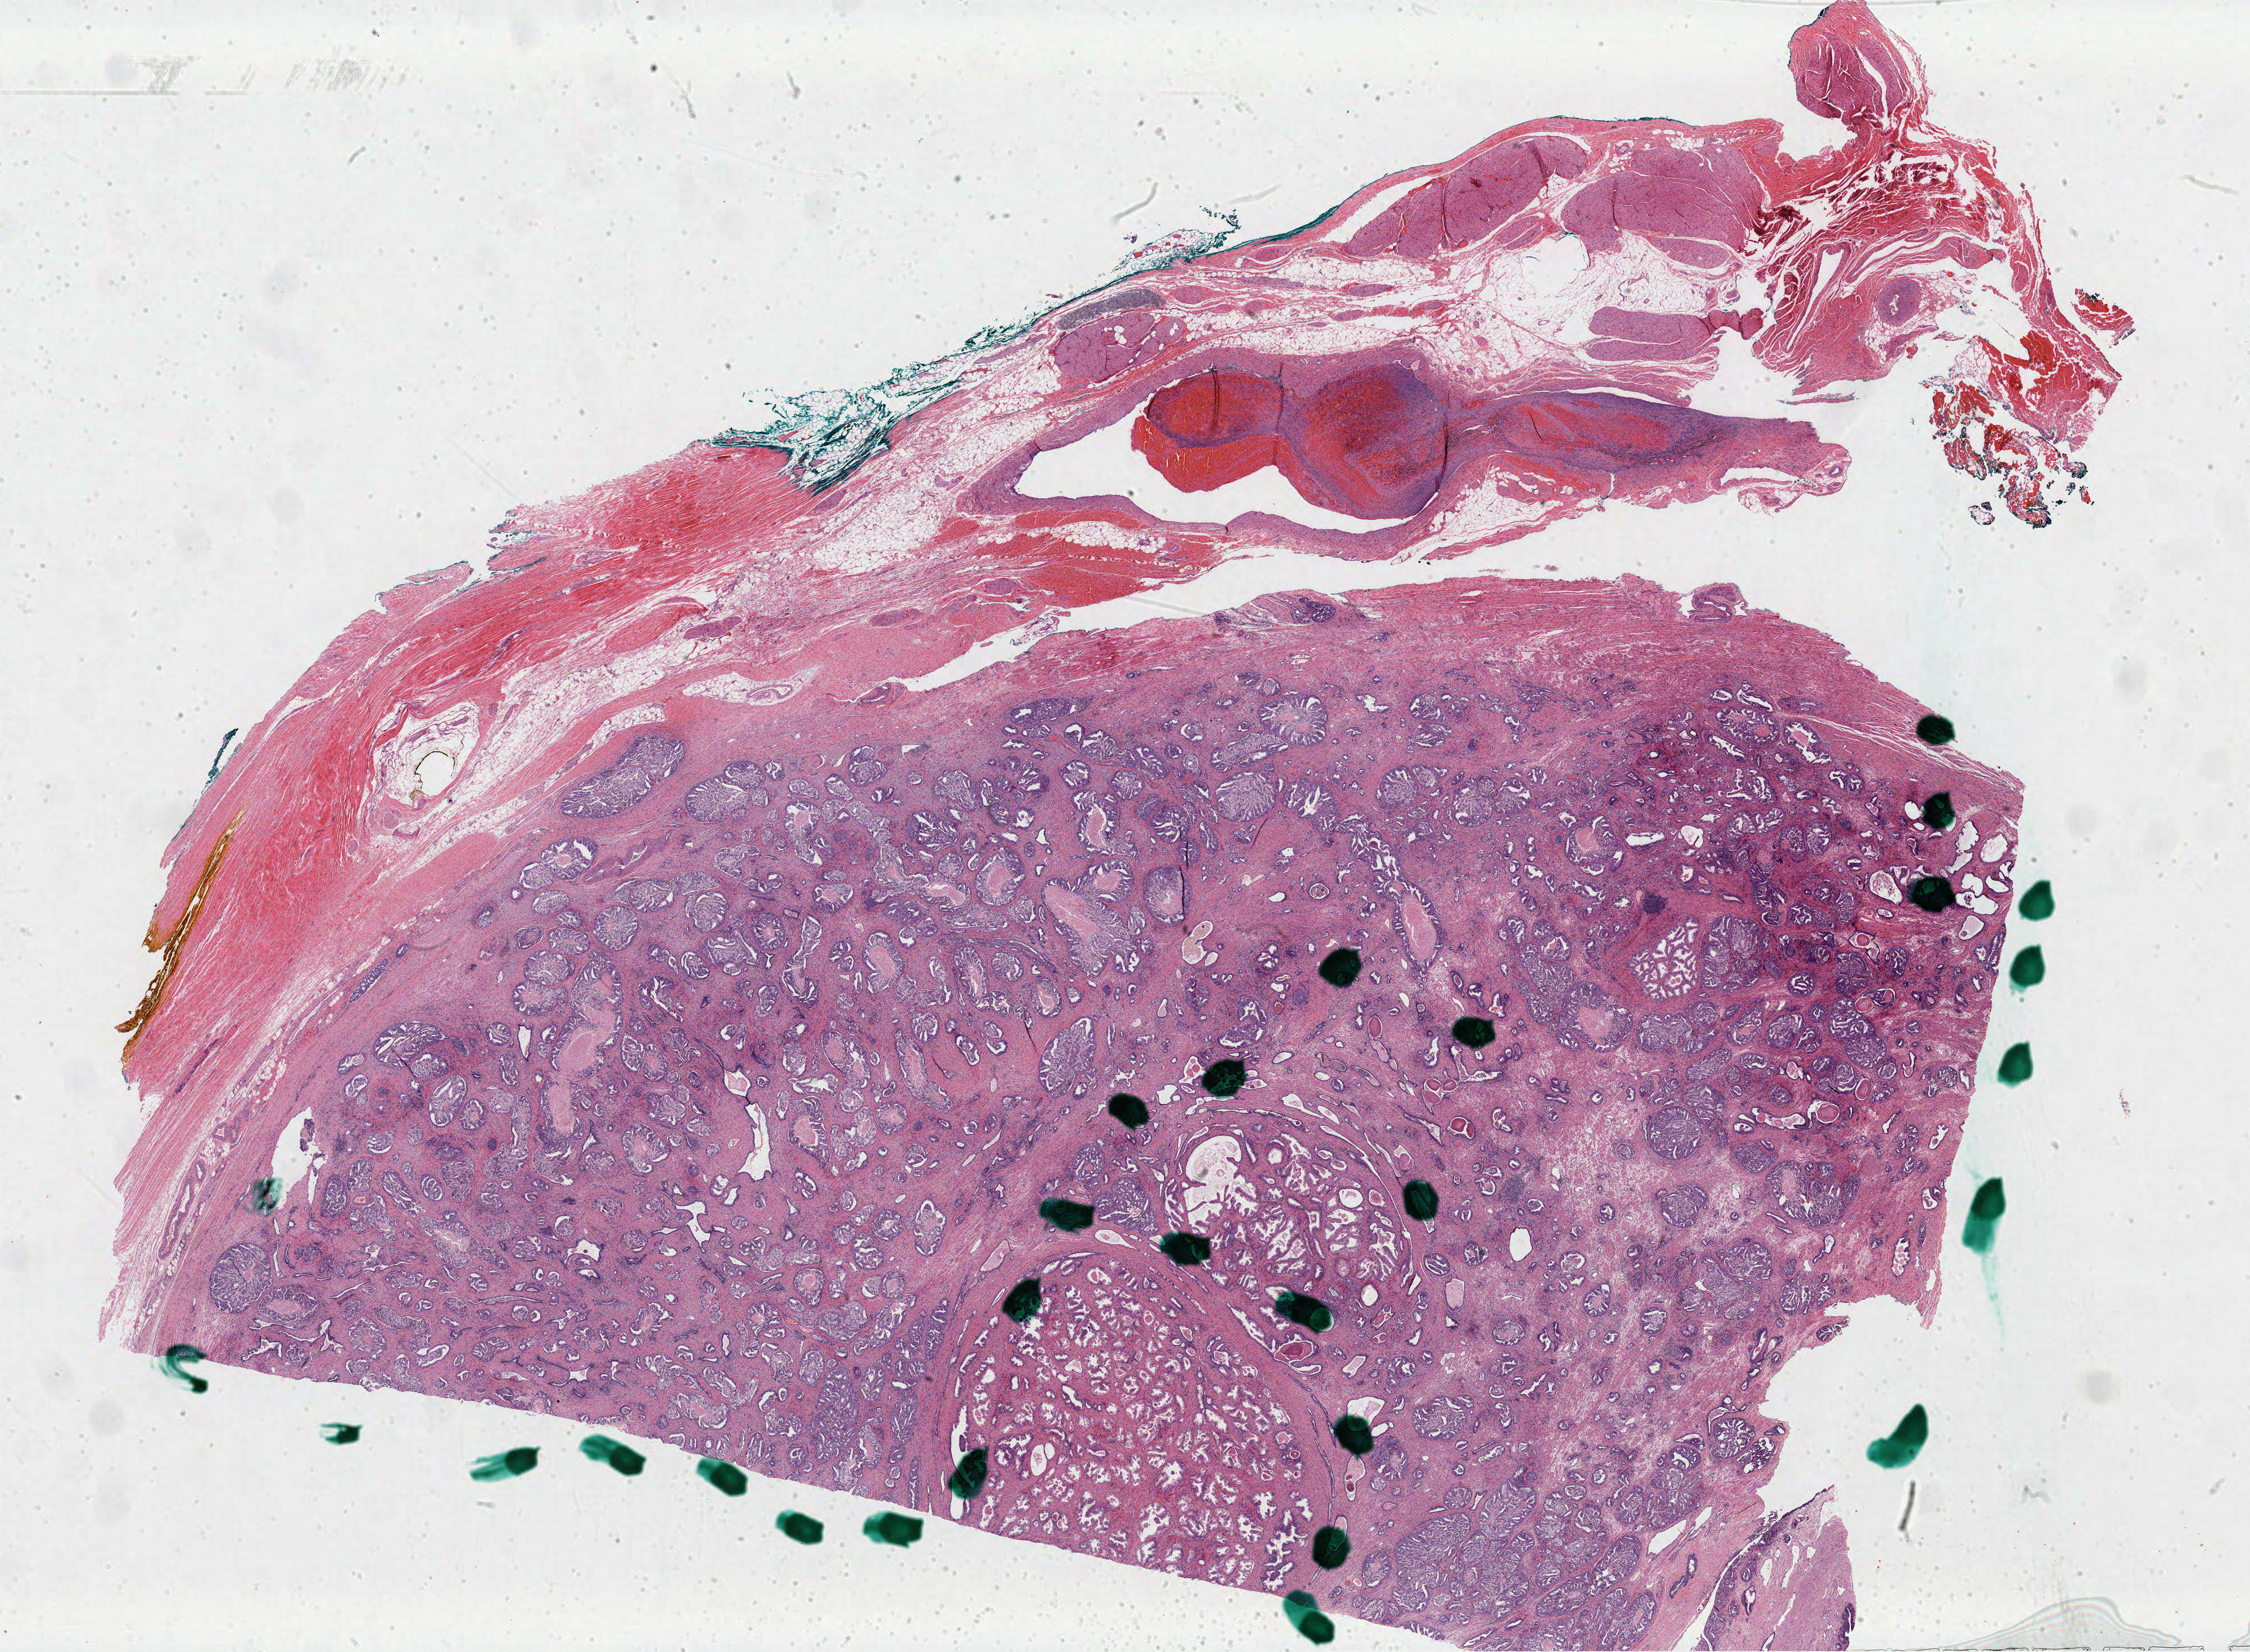
Whole-slide histology image, Hematoxylin and eosin (H&E) stained — a low-resolution overview of the entire scanned area, about 31.5 x 23.1 mm (slide scanned at 40x), formalin-fixed paraffin-embedded (FFPE) diagnostic section, sample: primary tumour, prostate. Male patient; age at initial diagnosis 57 years. Gleason score: 9 (4+5).
- histologic diagnosis: Adenocarcinoma, NOS
- lymph nodes positive (case pathology): 5 of 24 examined